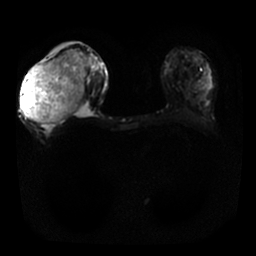
Breast MRI, one axial slice; slice 7 of 25 in the series (ordered by position); diffusion-weighted series; image 2 of 4 stored at this slice position (different b-values; order by instance number); 1.5 T; 4 mm slice thickness; 256 × 256 image matrix, field of view 340 × 340 mm. Female patient.
Outlined on this slice (outlined manually by an expert reader):
- tumour on diffusion-weighted imaging: bounding box [x1, y1, x2, y2] px = [22, 52, 86, 125]